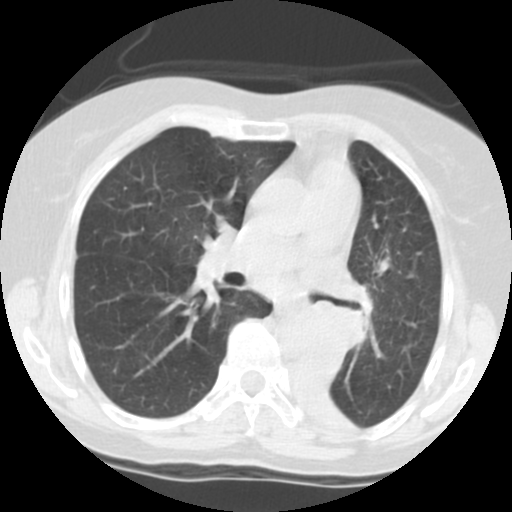
Axial slice from a low-dose chest CT screening exam. Third screening round (two years after baseline). Lung window (W 1500 / L -600 HU). 2.5 mm slice thickness. Female participant, aged 56 years at enrolment. Former smoker at enrolment.
Expert reader's lesion annotation, box from (x=314, y=295) to (x=372, y=348) px. No non-calcified nodule or mass ≥4 mm was recorded by the screening reader at this exam.